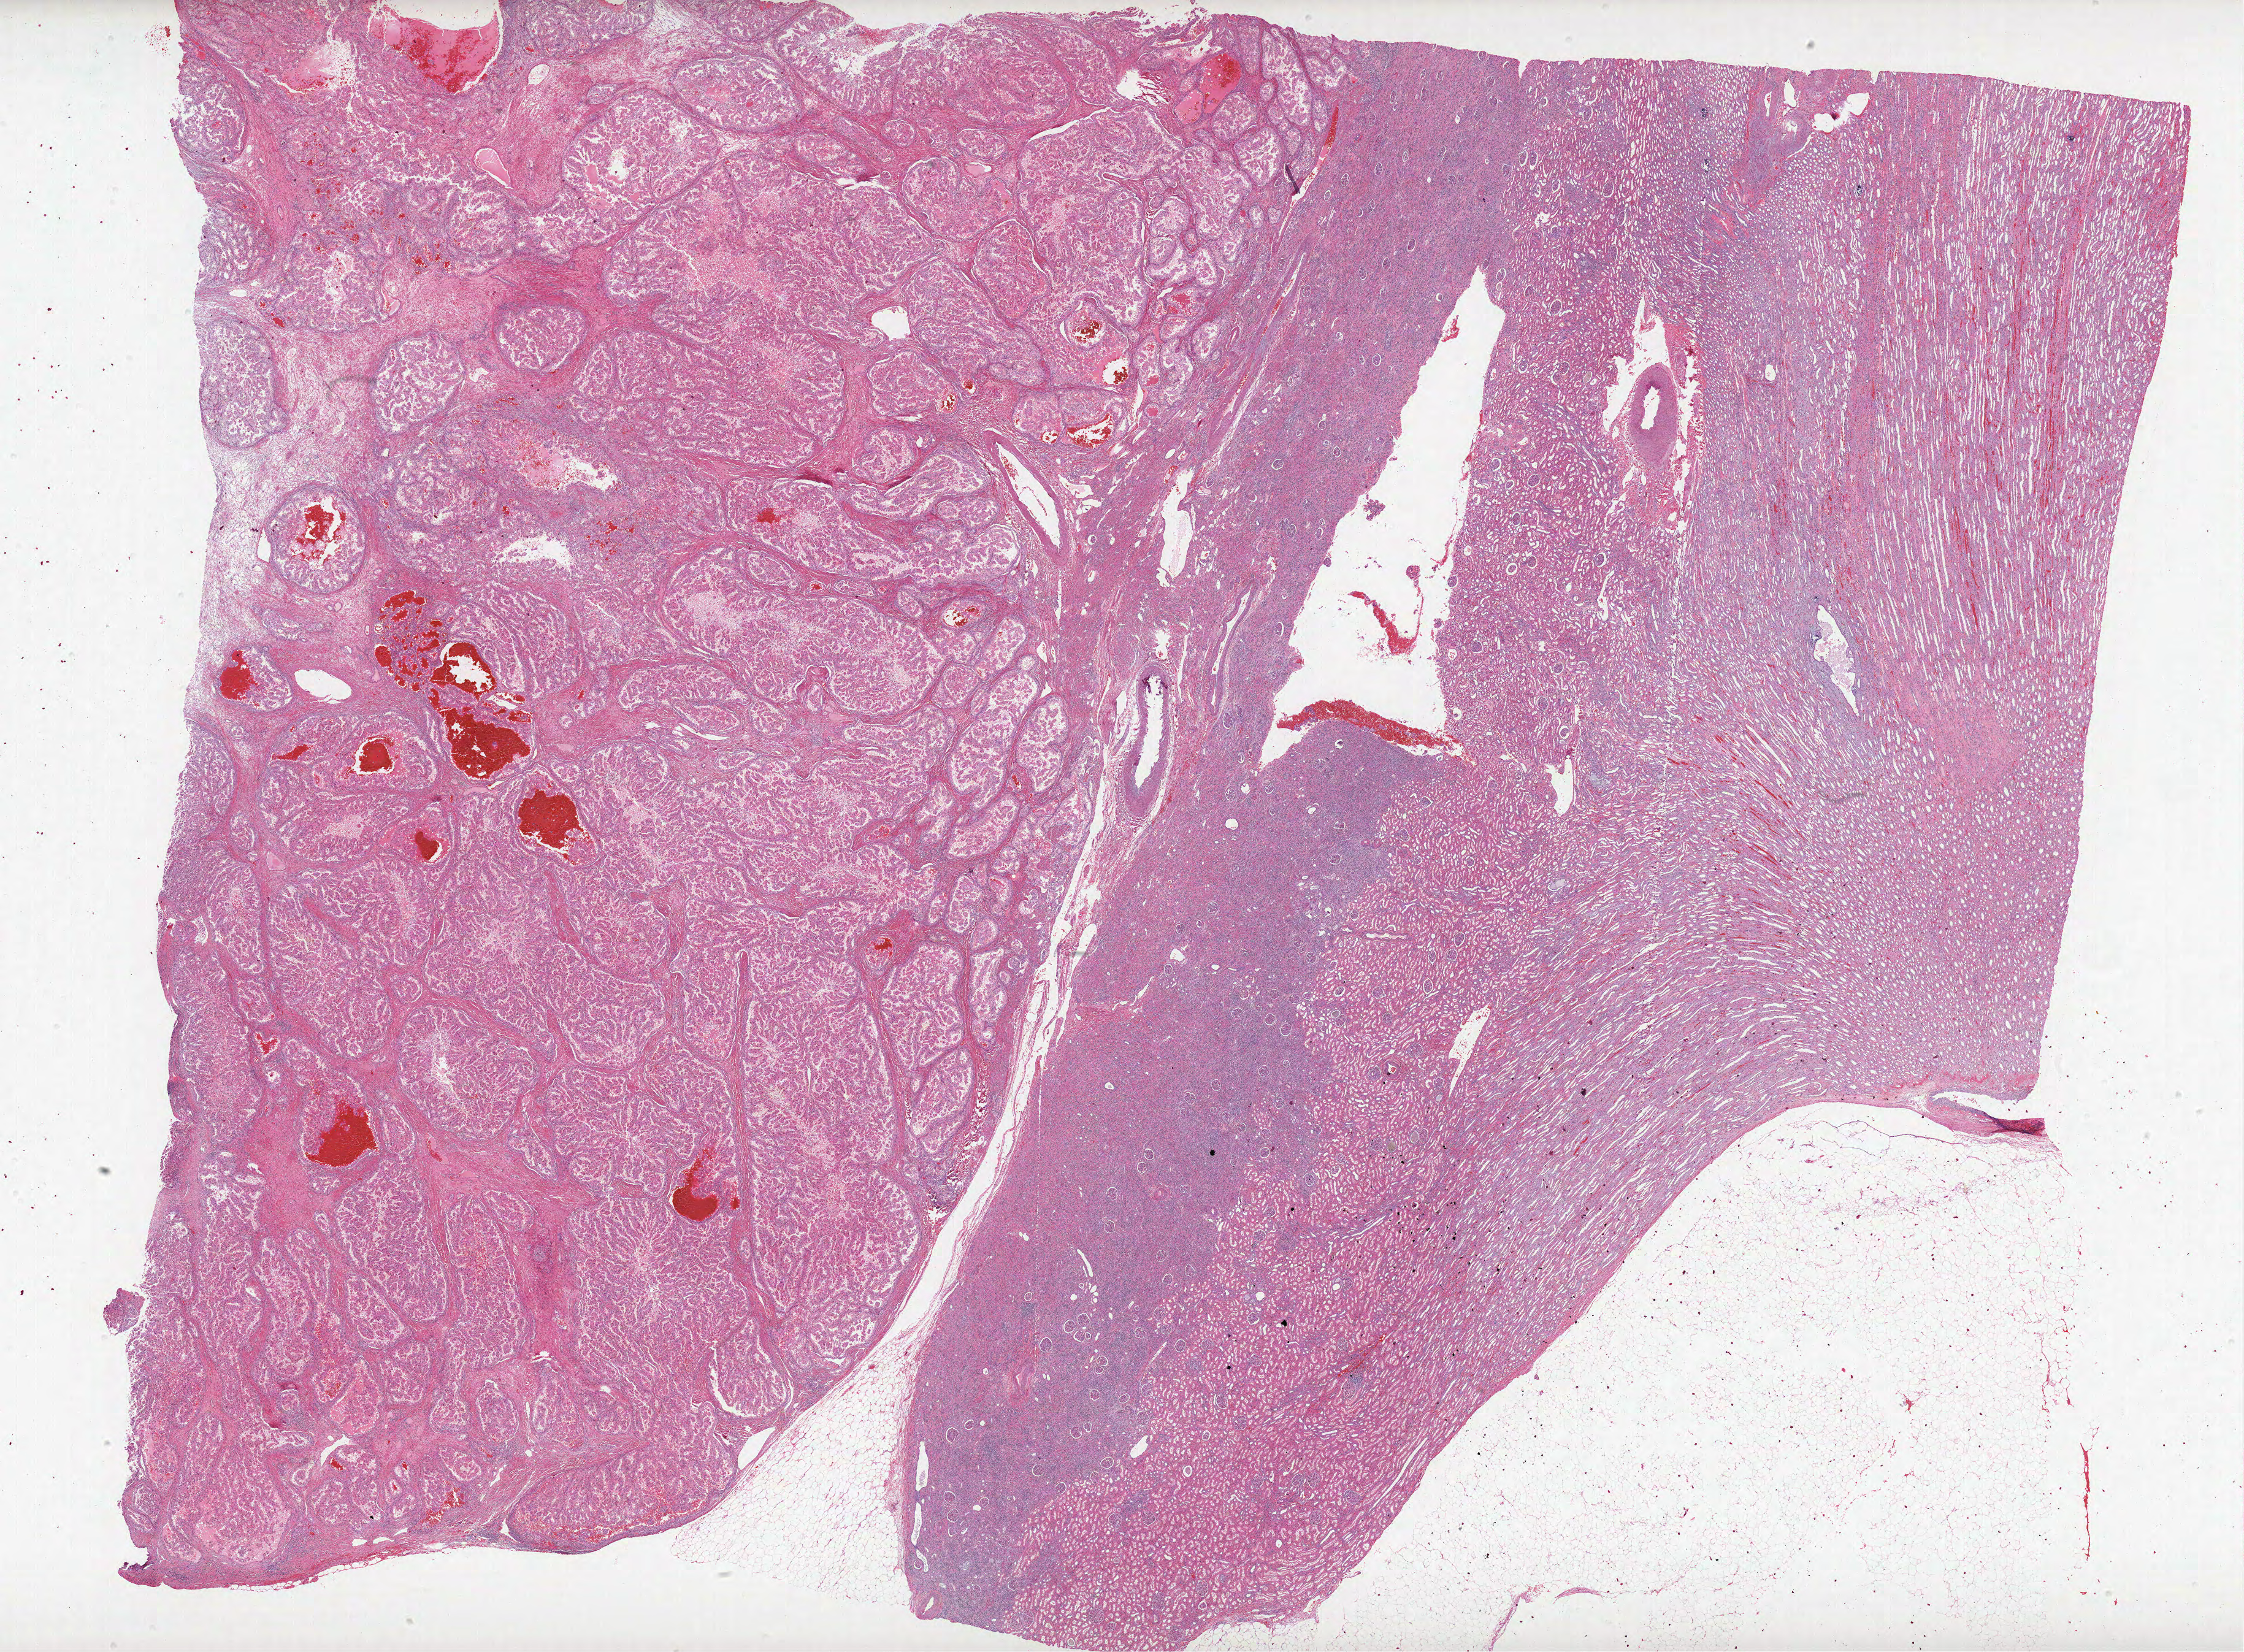
Digitized H&E tissue section (whole slide), shown as a low-resolution overview of the whole scanned area (about 29.3 x 21.5 mm), formalin-fixed paraffin-embedded (FFPE) diagnostic section, primary tumour sample from the kidney. Male patient; age at initial diagnosis 51 years.
Laterality: left. AJCC pathologic stage: I. Lymph nodes positive (case pathology): 0 of 21 examined. Histologic diagnosis: Papillary adenocarcinoma, NOS.